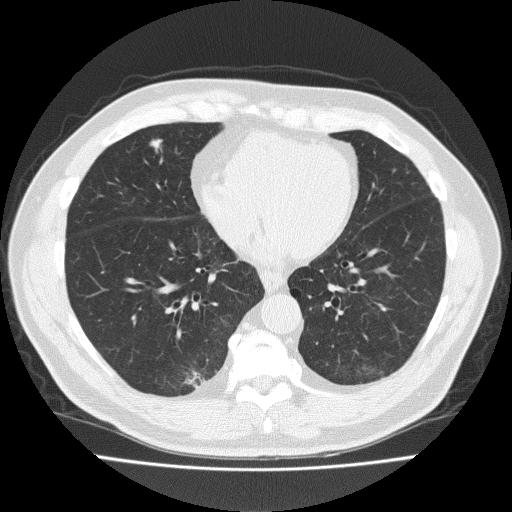
Low-dose screening chest CT, axial slice, second screening round (one year after baseline), lung window (W 1500 / L -600 HU), 2 mm slice thickness, slice 117 of 184 in the series, 512 × 512 image matrix. Male, age 57 years at enrolment.
Expert-annotated lung lesion, box from (x=133, y=131) to (x=176, y=169) px. The exam's reader record, not a measurement of the box and not confirmed to be the same lesion: non-calcified nodule or mass ≥4 mm, right middle lobe, 8 × 7 mm, spiculated (stellate) margins, soft tissue attenuation, pre-existing on the prior screen: yes; interval growth: yes.